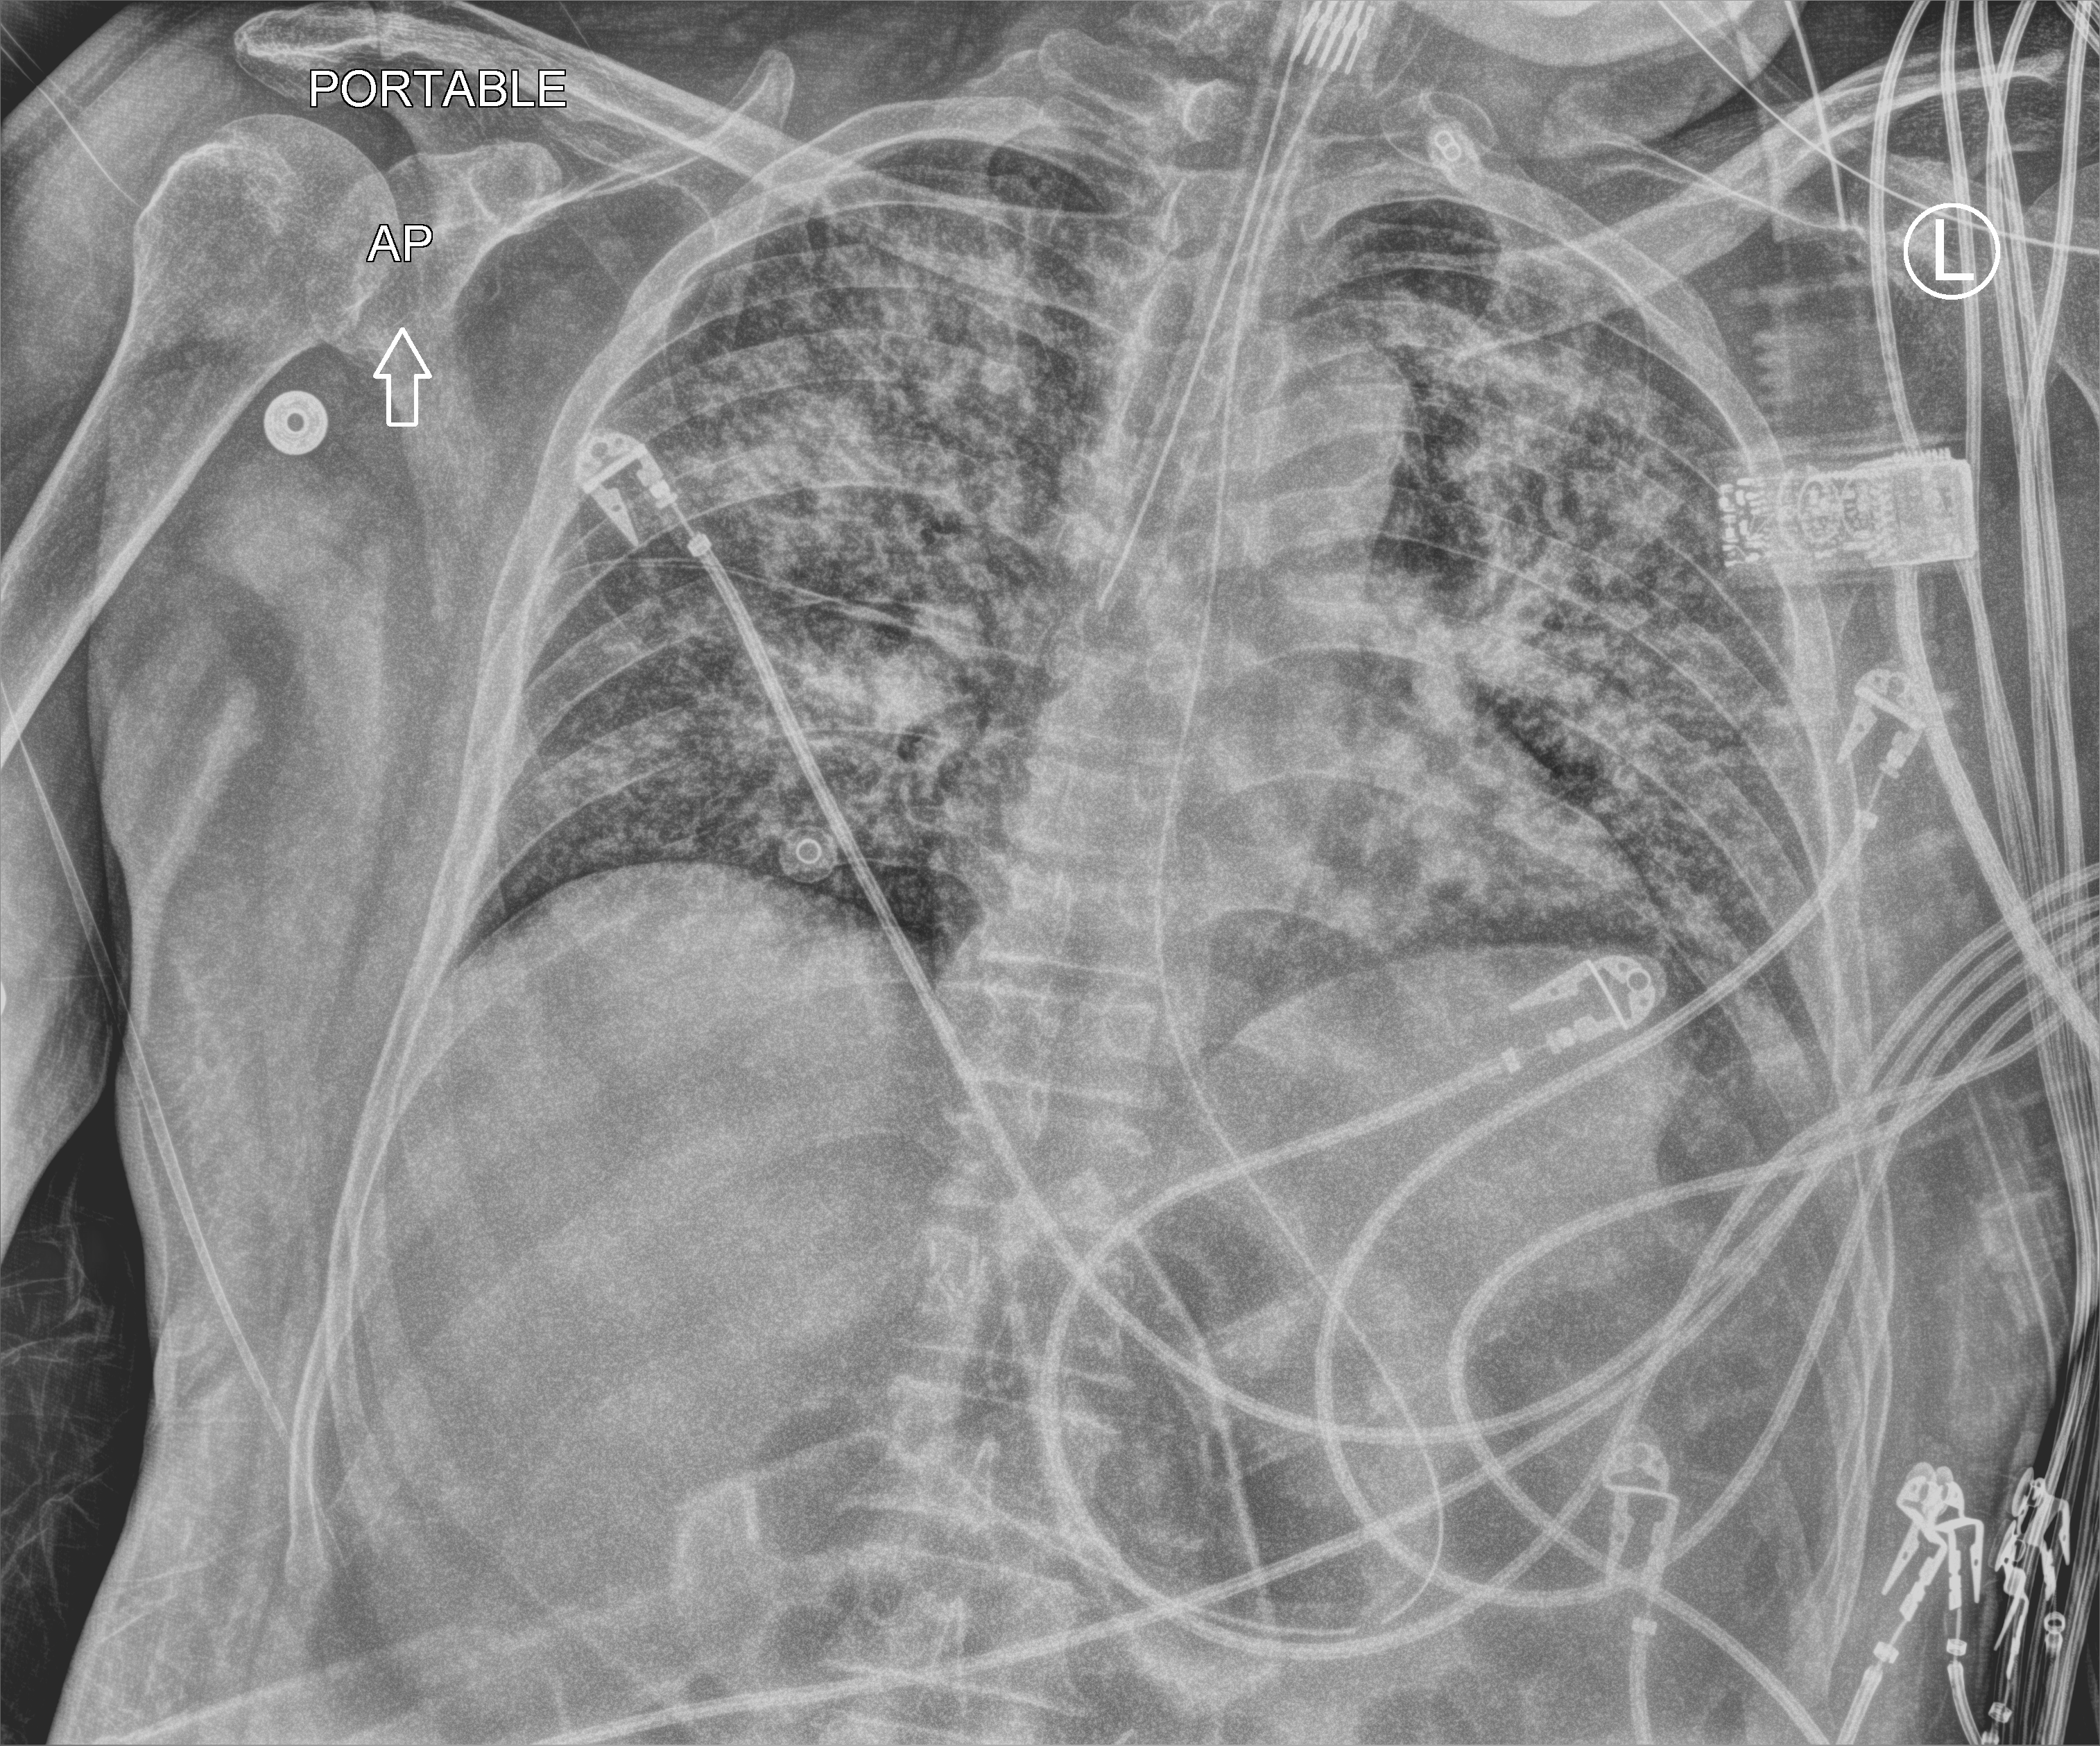
Portable chest radiograph, anteroposterior (AP) projection. Patient hospitalised with COVID-19; male, aged 60–74 years.
Hospital-stay facts (about this admission, not read from this image; timing relative to this image not recorded):
- admitted to intensive care during this hospital stay: yes